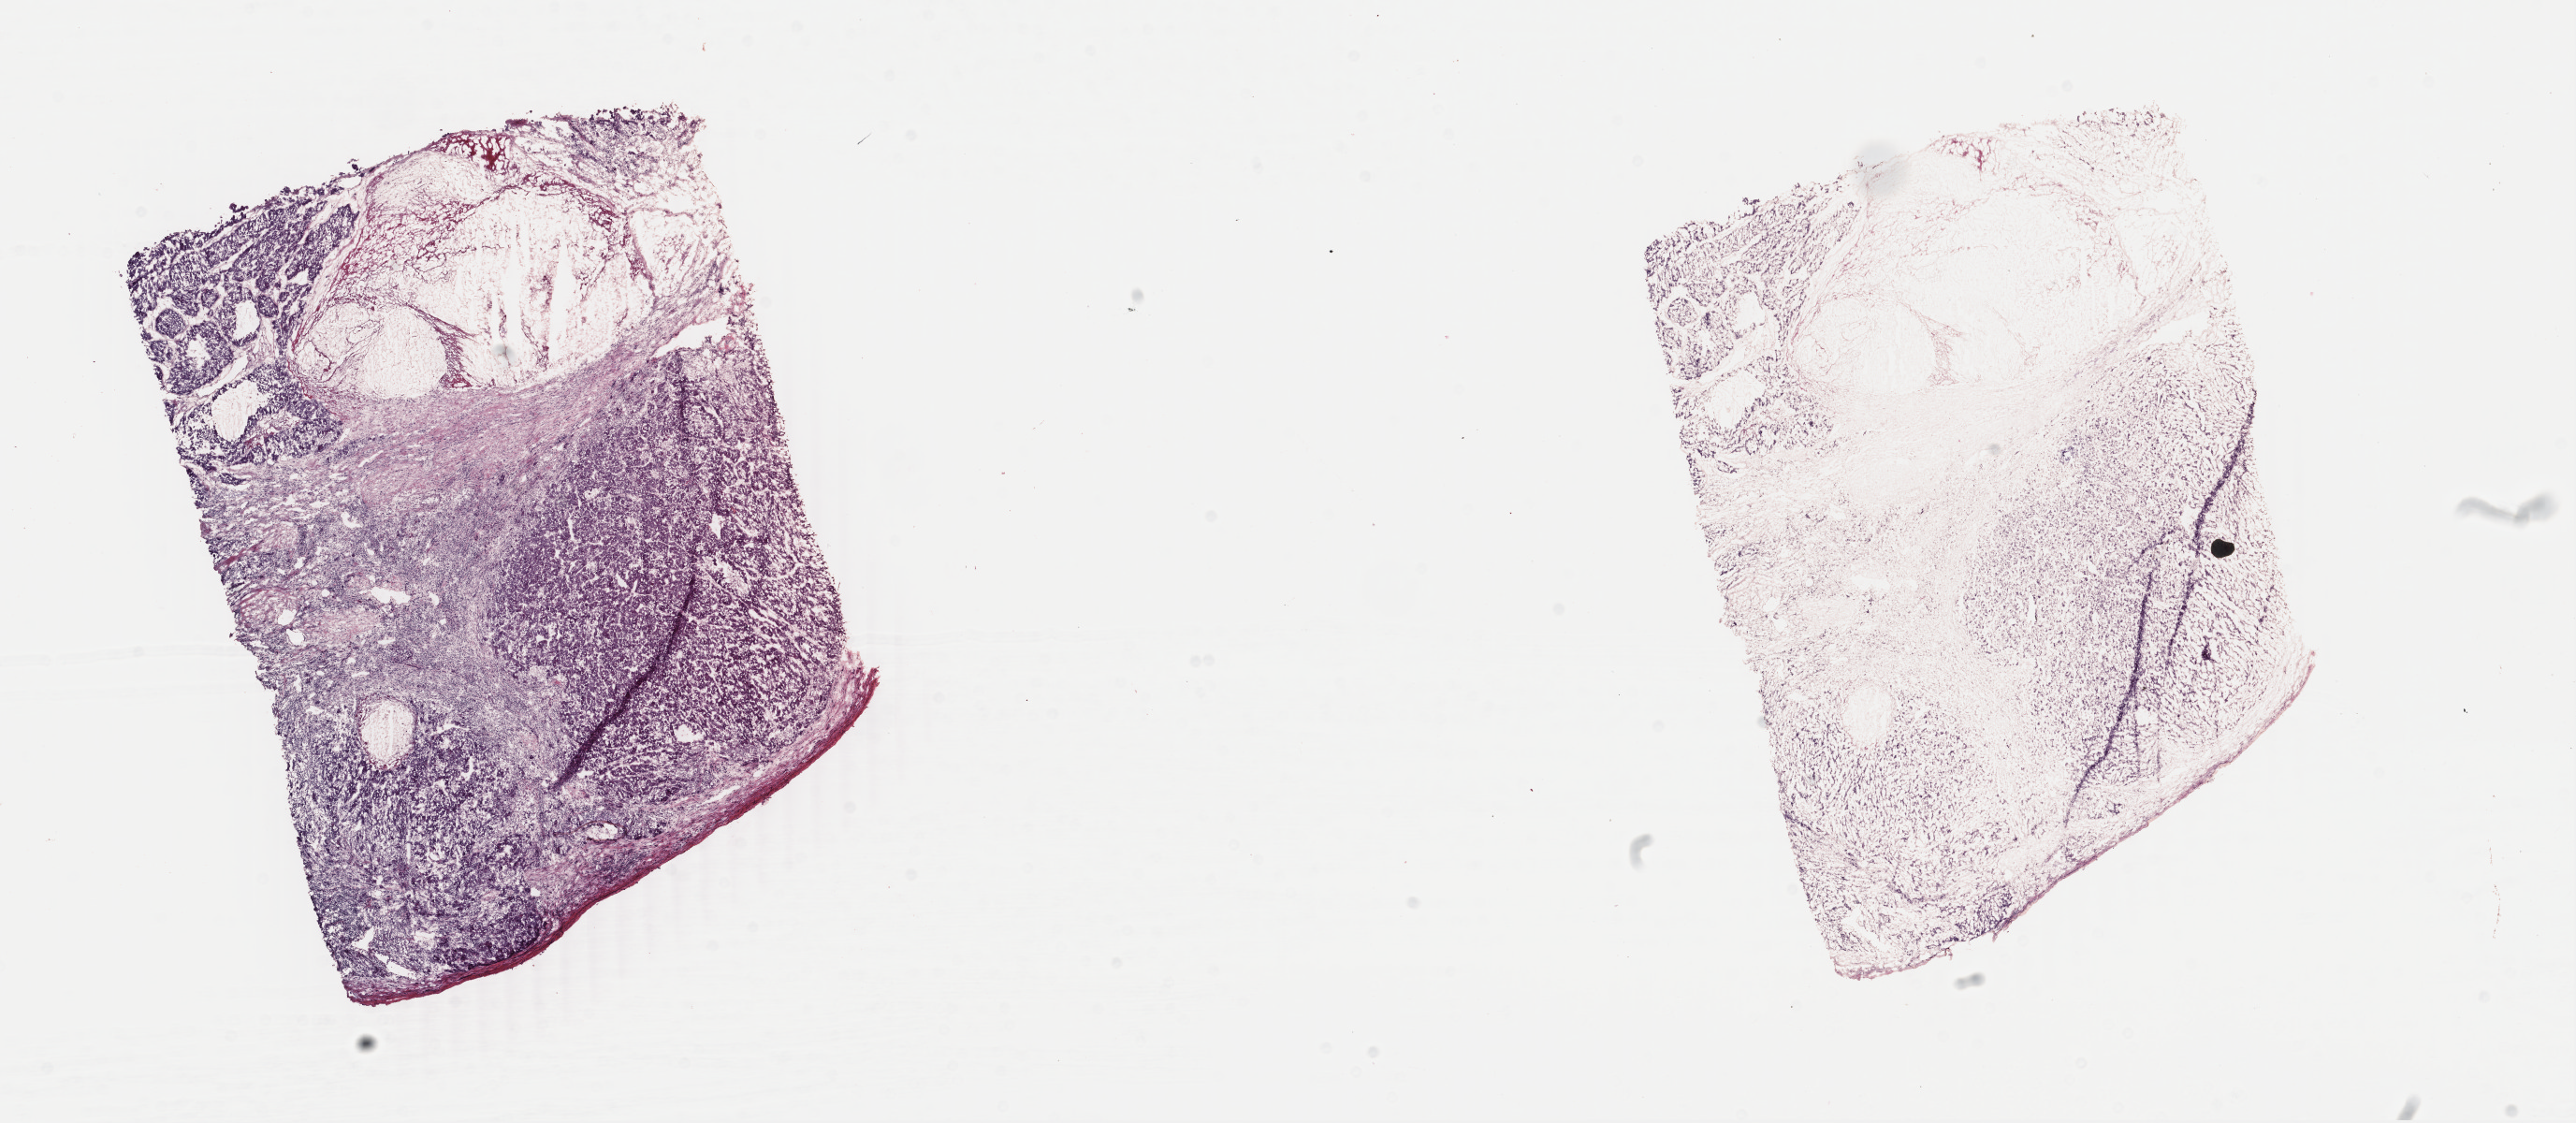
Digitized H&E-stained tissue section (whole slide), shown as a low-resolution overview of the whole scanned area (about 21.9 x 9.5 mm, from a 40x scan). Frozen section. Sample: primary tumour, liver. Patient: female, age at initial diagnosis 85 years. Histologic grade: G3 (poorly differentiated). Slide review estimates, as recorded: tumour cells 70%, tumour nuclei 60%, normal cells 0%, stromal cells 15%, necrosis 15%. Infiltration values recorded for this section: lymphocyte infiltration 5%, monocyte infiltration 0%, neutrophil infiltration 0%.
• AJCC pathologic stage: I
• pathologic diagnosis: Hepatocellular carcinoma, NOS